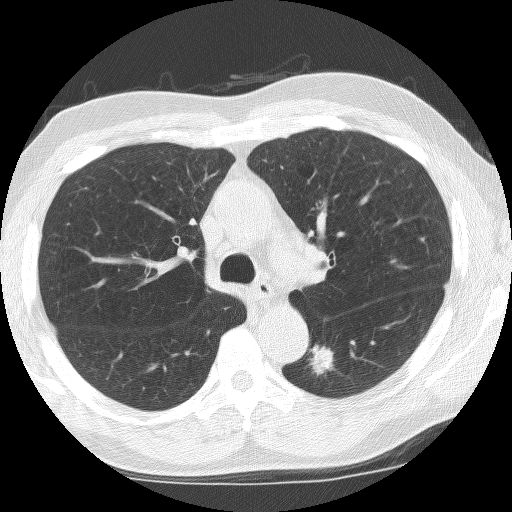
Low-dose screening chest CT, one axial slice. Position 100 of 155 along the scan axis. Reconstruction kernel BONE. Lung window (W 1500 / L -600 HU). 2.5 mm slice thickness. 512 × 512 image matrix, field of view 323 × 323 mm.
Structures marked on this image (expert manual segmentation):
- lesion 1 (tumor, lower lobe of left lung): bounding box [x1, y1, x2, y2] px = [309, 344, 334, 376]